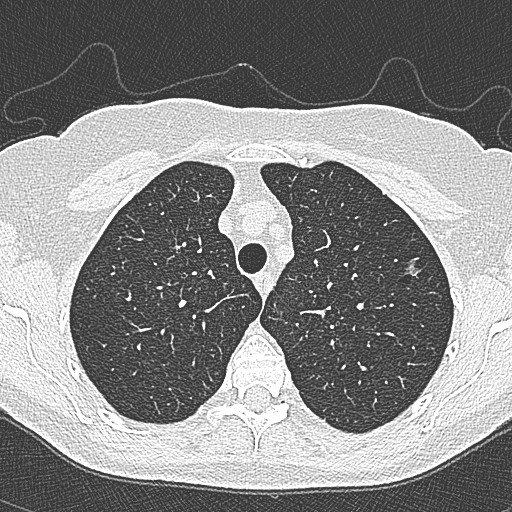
Low-dose screening chest CT, axial slice, second screening round (one year after baseline), lung window (W 1500 / L -600 HU), 1 mm slice thickness, 512 × 512 image matrix, field of view 298 × 298 mm. Female, age 65 years at enrolment. Current smoker at enrolment.
Lesion marked by an expert reader, bounding box [x1, y1, x2, y2] px = [394, 251, 432, 289]. The screening reader recorded 4 non-calcified nodules or masses ≥4 mm on this exam (left upper lobe, left upper lobe, left upper lobe, right lower lobe); which of them this box marks is not recorded. Official screen result: positive, change unspecified: nodule(s) >= 4 mm or enlarging nodule(s), mass(es), or other non-specific abnormalities suspicious for lung cancer.